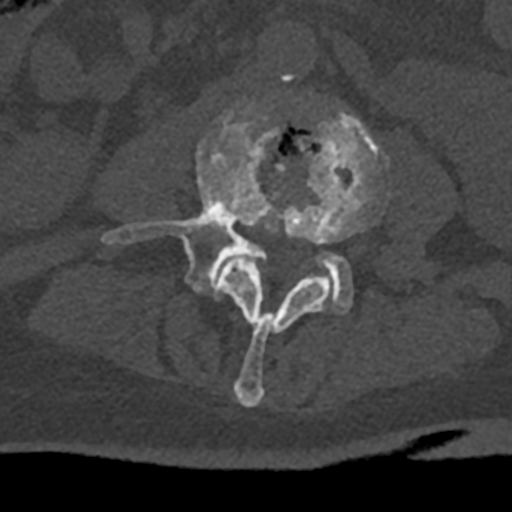
CT including the spine, one axial slice; position 289 of 797 along the scan axis; reconstruction kernel Br40s/3; bone window (W 1800 / L 400 HU); 512 × 512 image matrix, field of view 160 × 160 mm. Male patient, age 74 years. From the clinical record (not read from this slice): primary cancer: renal; vertebrae with lytic lesions (as recorded): T10, L1, L2, L3, L4, L5.
Annotated regions visible in this slice (semi-automatically segmented with operator editing):
- L3 vertebra: bounding box (x1, y1, x2, y2) in pixels: (218, 109, 389, 407)
- L4 vertebra: (102, 105, 353, 314)